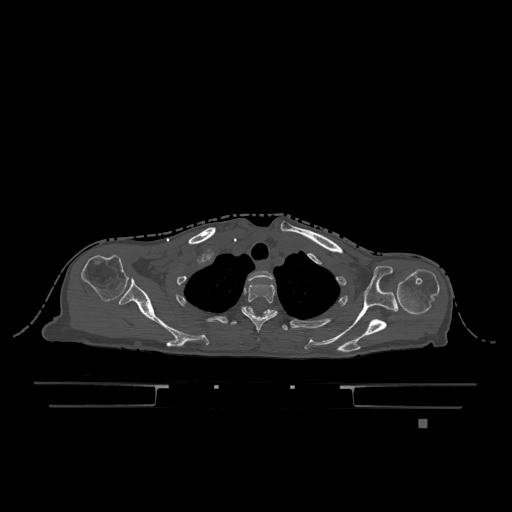
CT including the spine, one axial slice. Position 957 of 1317 along the scan axis. Bone window (W 1800 / L 400 HU). 512 × 512 image matrix, field of view 500 × 500 mm. Patient: female, 74 years. From the clinical record (not read from this slice): primary cancer: lung; vertebrae with lytic lesions (as recorded): T1, T4, T5, T6, L4, L5.
Structures marked on this image (semi-automatic segmentation, software-assisted and operator-edited):
- T1 vertebra: box from (x=248, y=271) to (x=273, y=281) px
- T2 vertebra: (x=241, y=283)–(x=278, y=333)
- T3 vertebra: (x=230, y=307)–(x=288, y=331)
- T6 vertebra: (x=244, y=306)–(x=276, y=314)